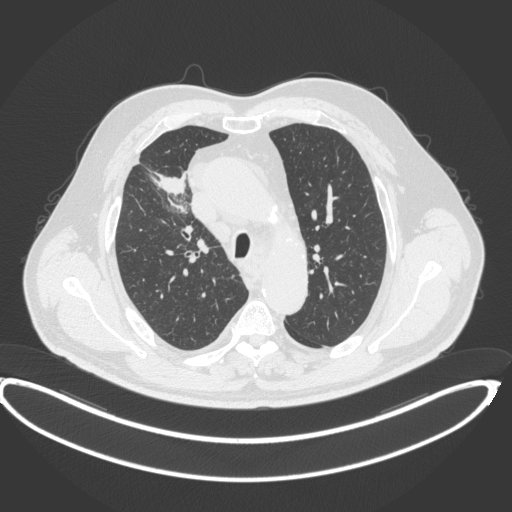
Chest CT, one axial slice. Reconstruction kernel B31f. 120 kVp. Lung window (W 1500 / L -600 HU). 1 mm slice thickness. 512 × 512 image matrix, field of view 448 × 448 mm. Male patient, age 62 years. Case-level facts recorded for this patient, not image findings: clinical TNM (as recorded): T1c N3 M1c.
Outlined on this slice (rectangle marked by the reading radiologist):
- lung tumour (recorded histology: adenocarcinoma): bounding box (x1, y1, x2, y2) in pixels: (152, 171, 188, 196)